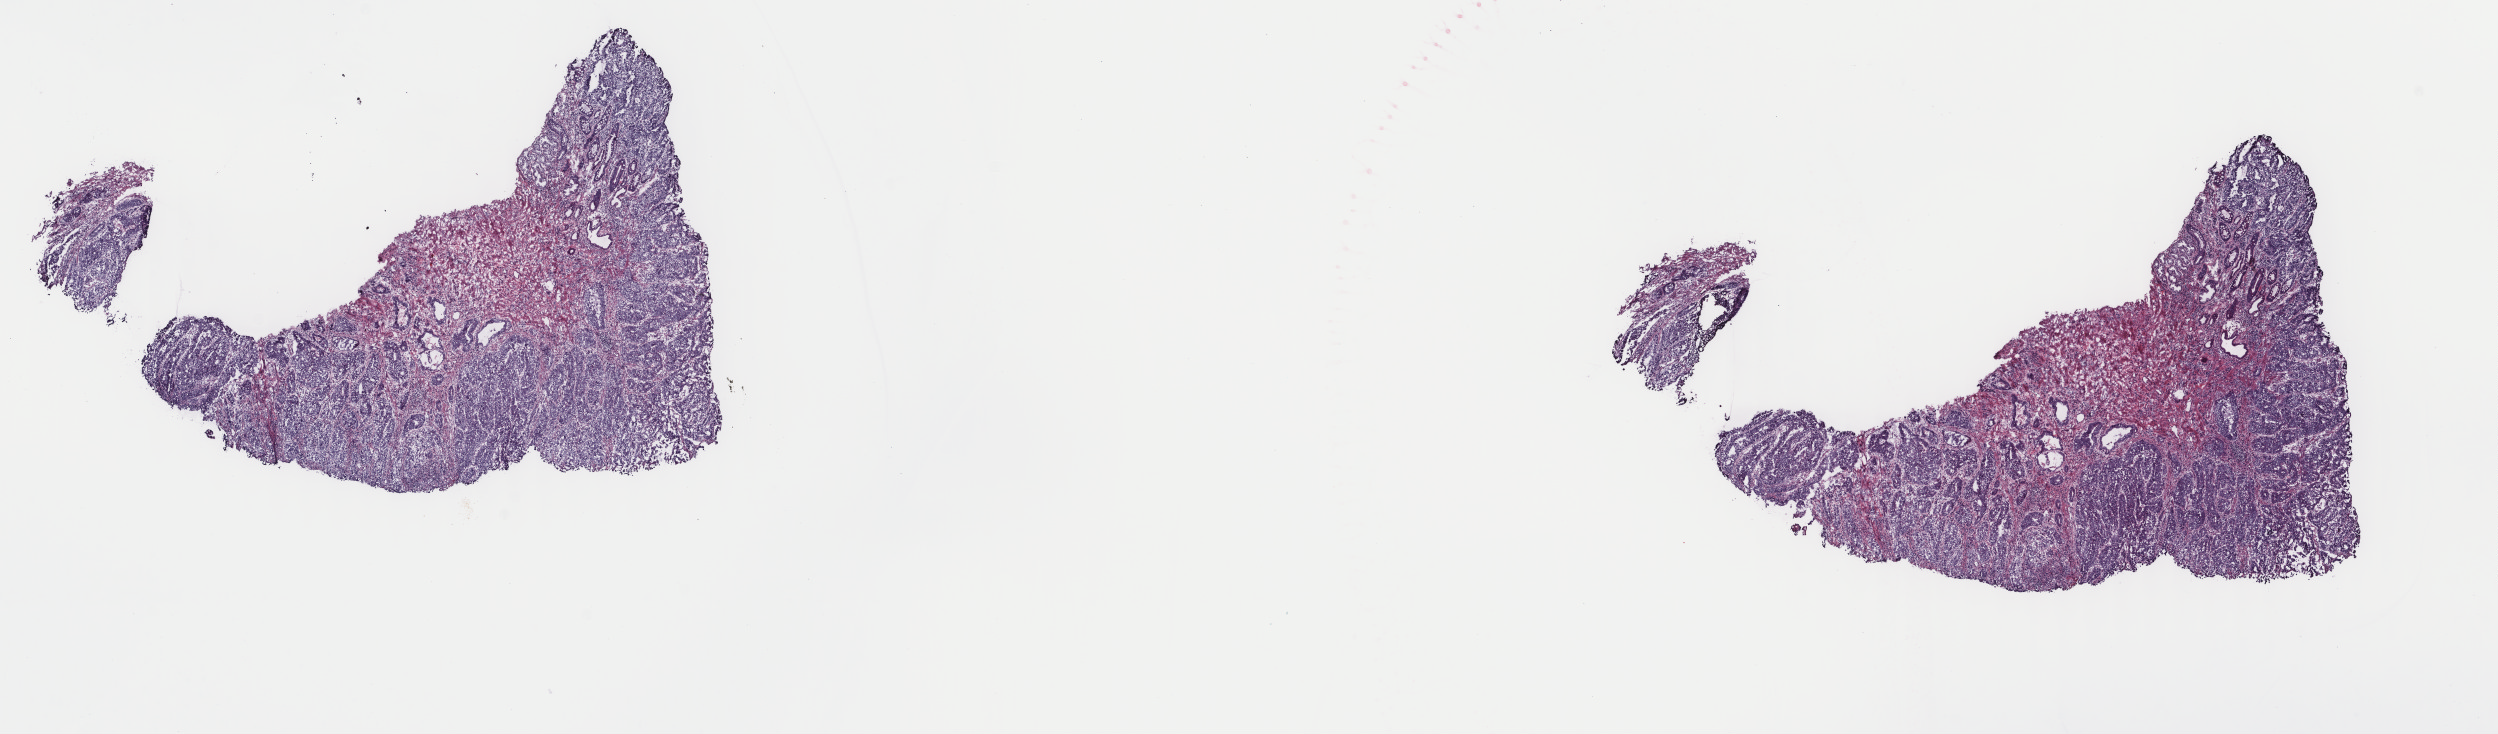
Digitized H&E-stained tissue section (whole slide), low-resolution overview of the scanned area, about 19.8 x 5.8 mm (from a 40x scan), frozen section from the top of the tissue portion, primary tumour sample from the stomach. Male, age 73 years at initial diagnosis. Histologic grade: G2 (moderately differentiated). Slide review estimates, as recorded: tumour cells 80%, tumour nuclei 70%, normal cells 20%, stromal cells 0%, necrosis 0%. Infiltration values recorded for this section: lymphocyte infiltration 3%, monocyte infiltration 1%, neutrophil infiltration 1%.
* AJCC pathologic stage: IIIA (7th edition)
* histologic diagnosis: Tubular adenocarcinoma (gastric antrum)
* lymph nodes positive (case pathology): 3 of 56 examined